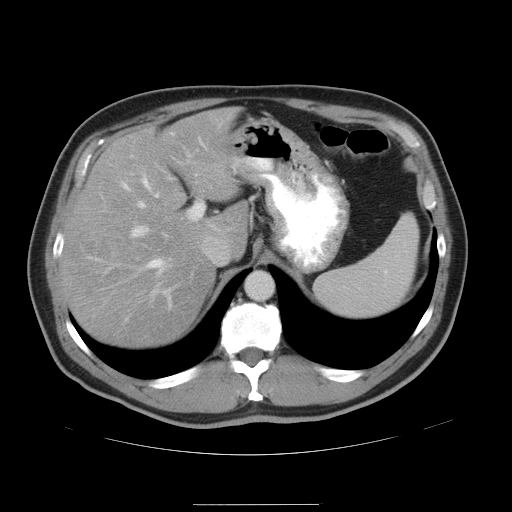
Contrast-enhanced abdominal CT, one axial slice. Slice 34 of 47 in the series (ordered by position). 120 kVp. Soft-tissue window (W 400 / L 40 HU). 5 mm slice thickness. 512 × 512 image matrix, field of view 420 × 420 mm. Male patient, age 61 years. Case-level facts recorded for this patient, not image findings: diagnosis: colorectal cancer liver metastases, imaged before liver resection; multiple liver metastases: no; largest metastasis: 1.2 cm; disease in both lobes: no.
Annotated regions visible in this slice (manually delineated by an expert):
- hepatic veins: bounding box (x1, y1, x2, y2) in pixels: (123, 132, 204, 297)
- liver: (62, 108, 250, 348)
- planned liver remnant (the part of the liver to remain after resection): (62, 108, 250, 348)
- portal vein (with intrahepatic branches): (120, 203, 204, 297)